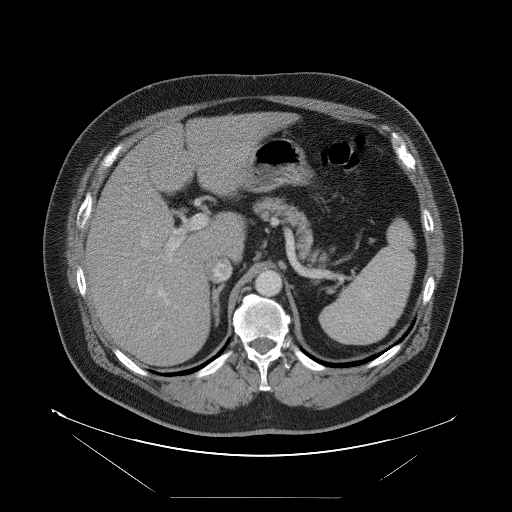
Contrast-enhanced abdominal CT, one axial slice; 120 kVp; soft-tissue window (W 400 / L 40 HU); 5 mm slice thickness; 512 × 512 image matrix. Male patient, age 61 years. From the clinical record (not read from this slice): diagnosis: colorectal cancer liver metastases, imaged before liver resection; multiple liver metastases: no; largest metastasis: 6.5 cm.
Annotated regions visible in this slice (outlined manually by an expert reader):
- hepatic veins: bounding box (x1, y1, x2, y2) in pixels: (141, 231, 148, 247)
- liver: (86, 113, 288, 367)
- planned liver remnant (the part of the liver to remain after resection): (145, 113, 287, 253)
- portal vein (with intrahepatic branches): (157, 214, 206, 302)